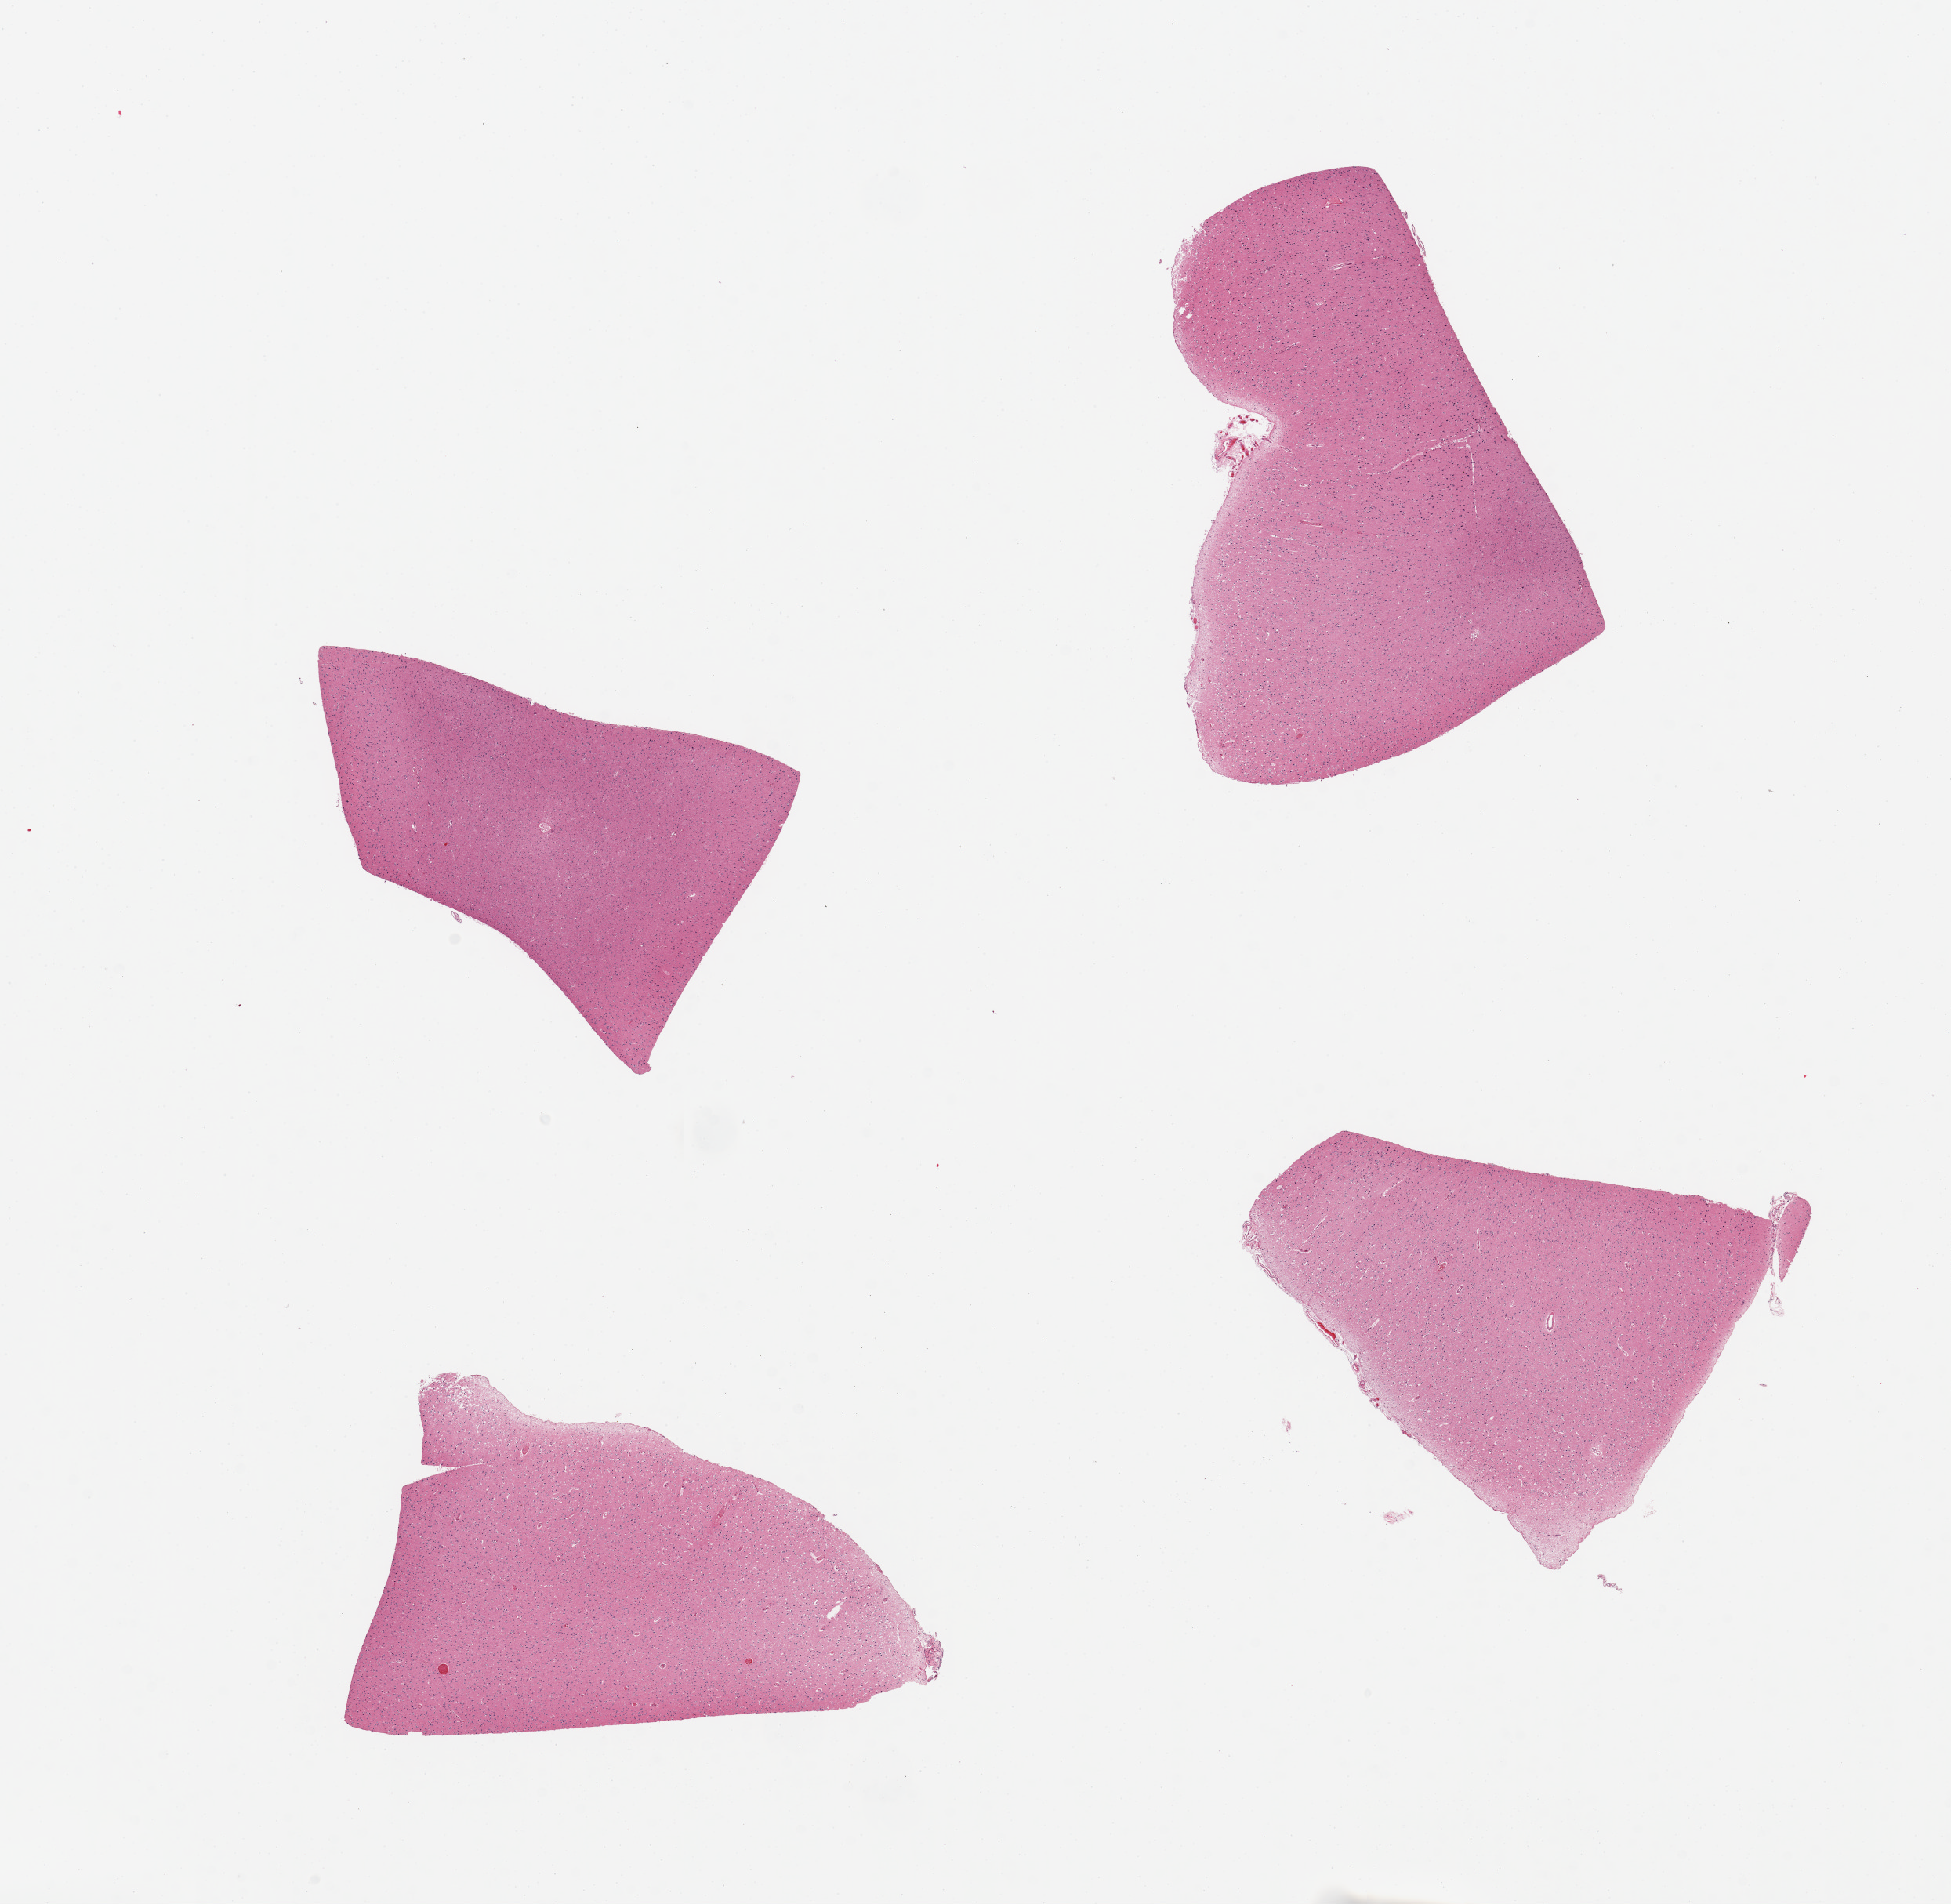
Hematoxylin and eosin (H&E) whole-slide image — whole scanned area (about 19.7 x 19.2 mm, acquisition: 20x scan) shown as a low-resolution overview; PAXgene-fixed, paraffin-embedded tissue; target tissue: cerebral cortex; tissue donor sample. Female donor.
Pathologist's review note for this sample: 4 pieces, modertely autolyzed.